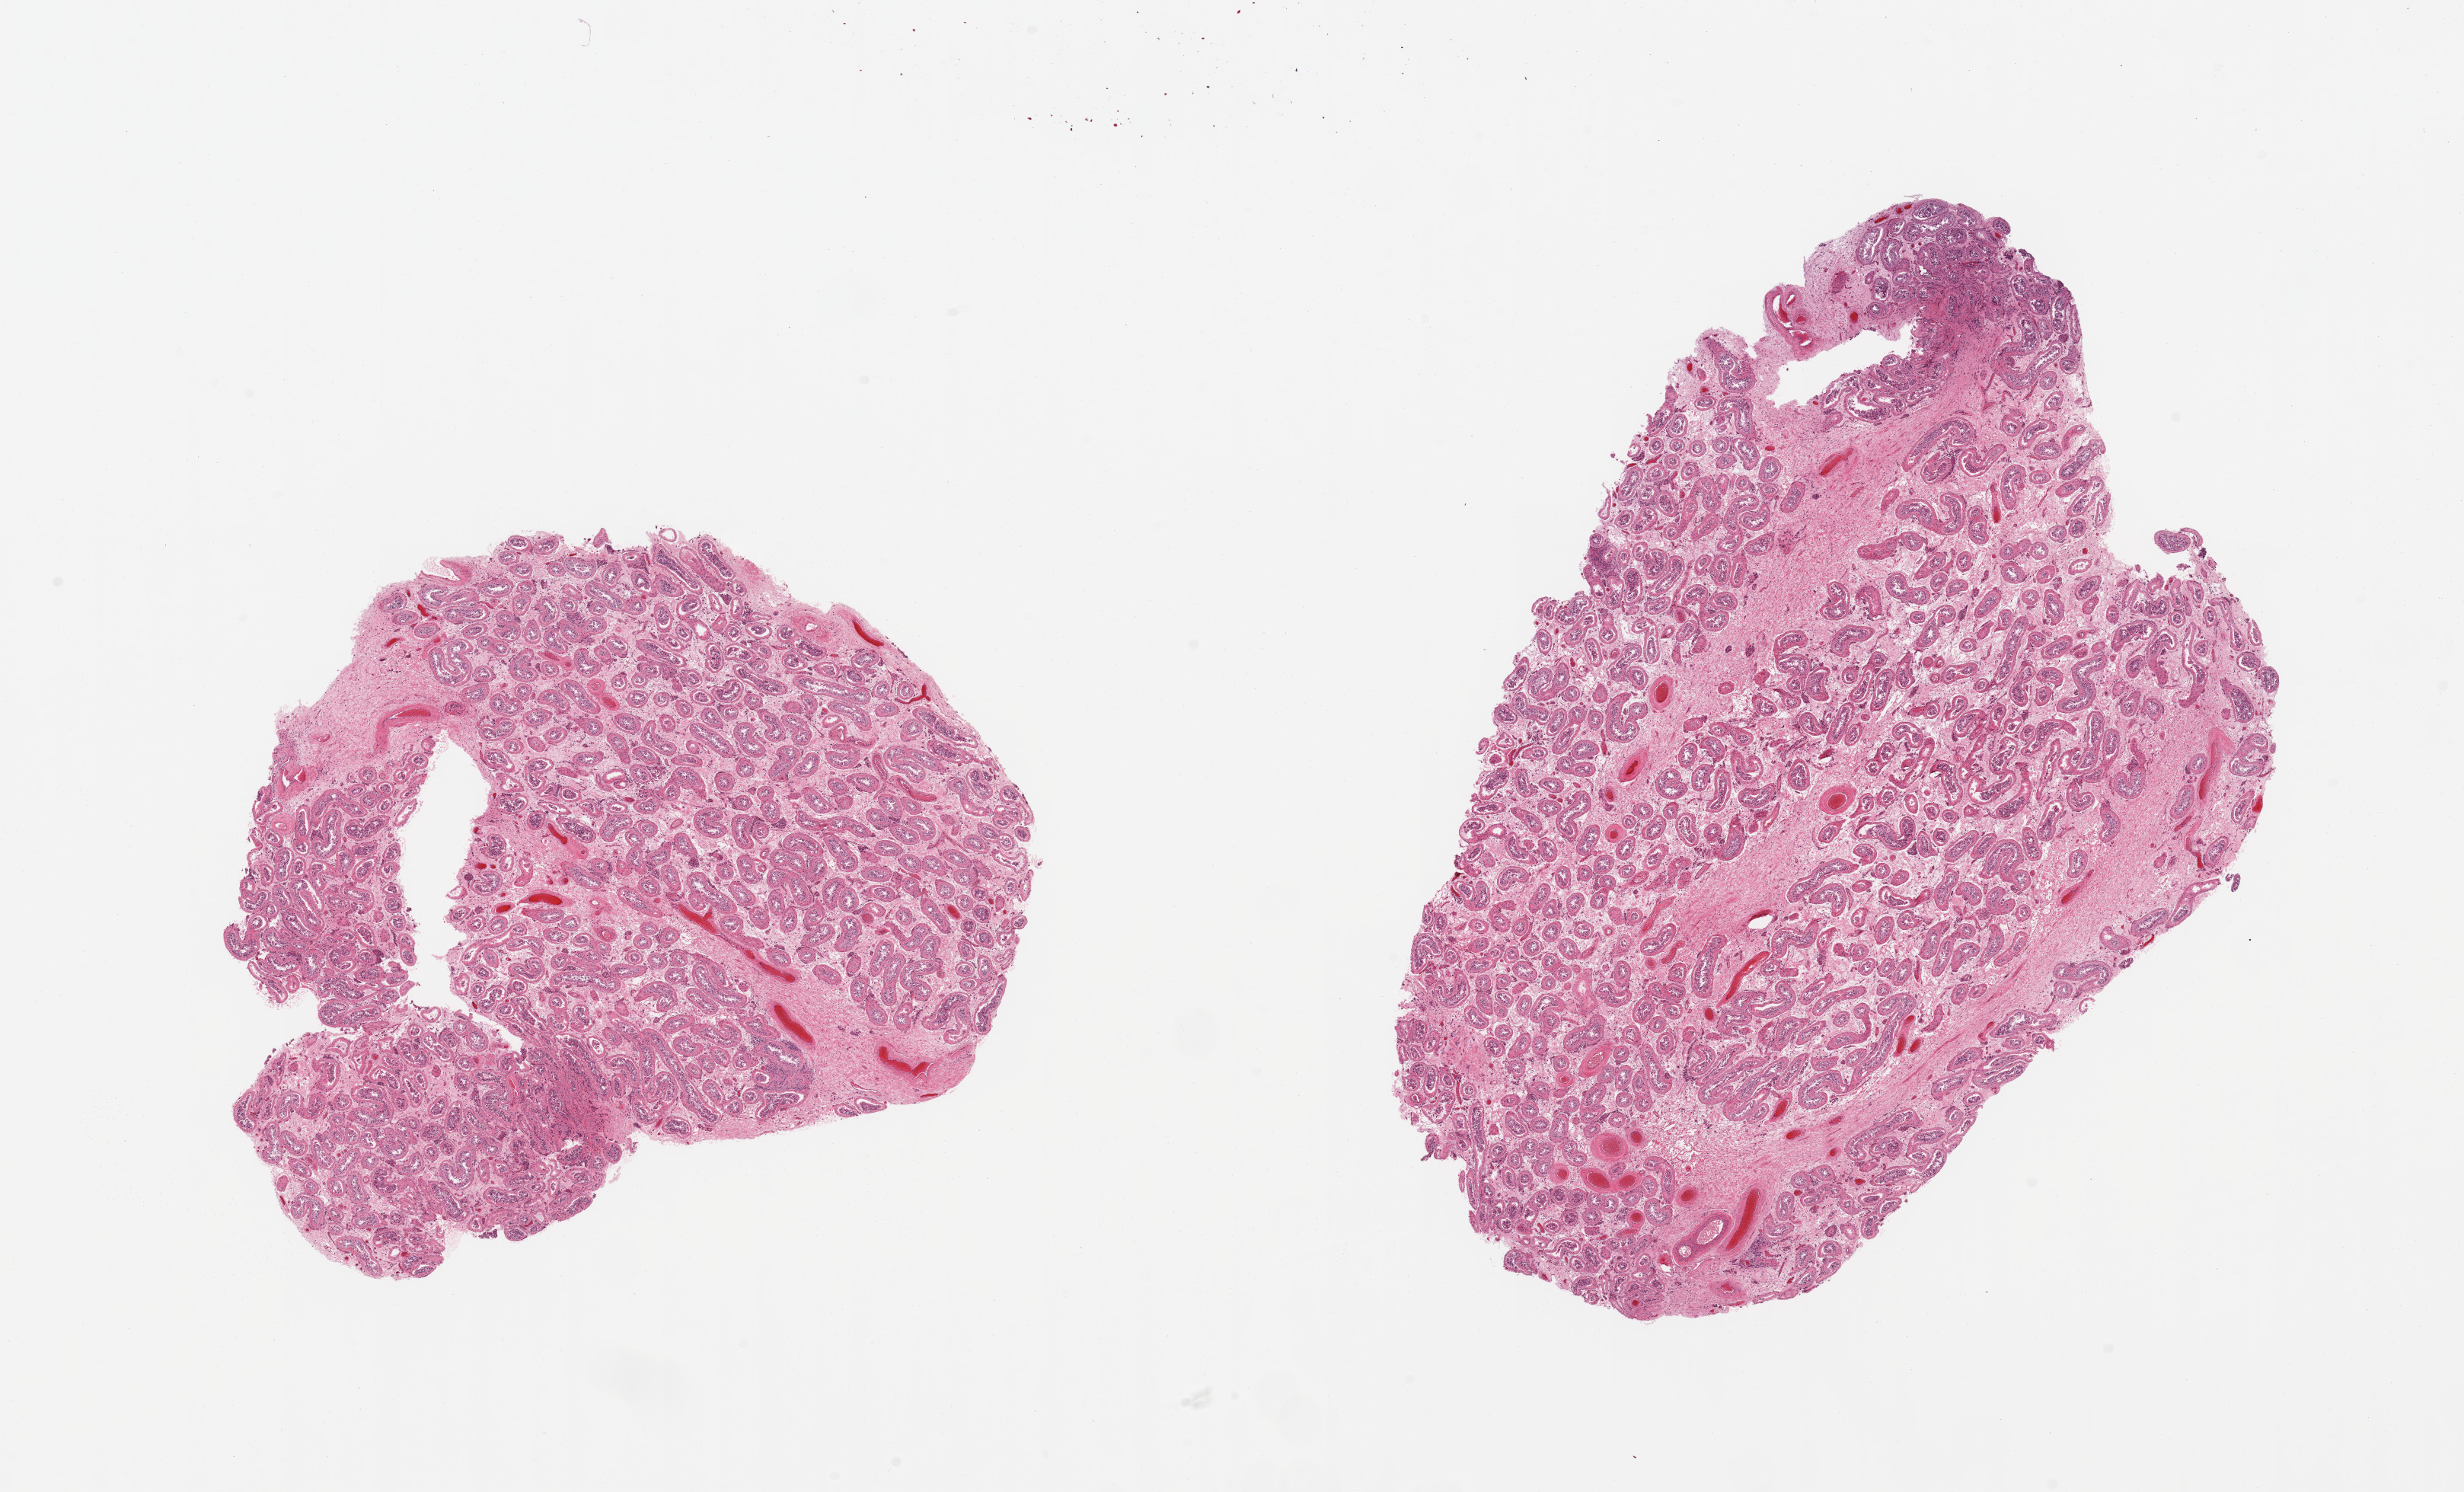
Whole-slide image, H&E stain, shown as a low-resolution overview of the whole scanned area (about 25.6 x 15.5 mm). PAXgene-fixed, paraffin-embedded tissue. Sampled site (target tissue): testis. Tissue donor sample. Donor: male.
Pathologist's review note for this sample: 2 pieces, diffusely atrophic, absent spermatogenesis, Sertoli only appearance.